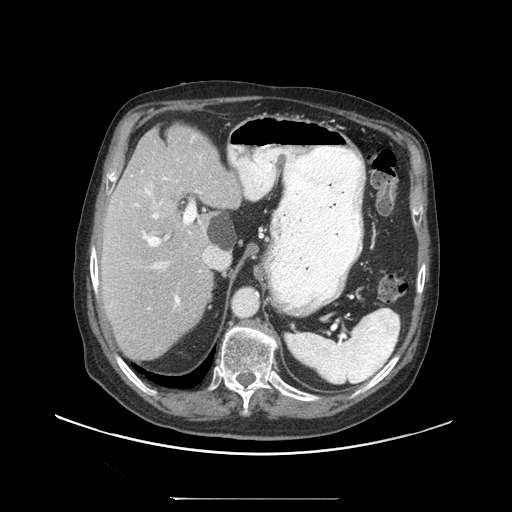
Contrast-enhanced abdominal CT (liver protocol), one axial slice. Slice 67 of 97 in the series (ordered by position). Reconstruction kernel STANDARD. 140 kVp. Soft-tissue window (W 400 / L 40 HU). 2.5 mm slice thickness. 512 × 512 image matrix, field of view 450 × 450 mm. Case-level facts recorded for this patient, not image findings: diagnosis: hepatocellular carcinoma (patient treated with transarterial chemoembolisation; whether this scan precedes or follows treatment is not stated here); TNM stage (as recorded): Stage-IIIC; Child-Pugh class: A; tumour differentiation: well differentiated.
Structures marked on this image (semi-automatically segmented with operator editing):
- abdominal aorta: bounding box [x1, y1, x2, y2] px = [233, 288, 257, 316]
- liver parenchyma outside the tumour (the mass and vessels are separate outlines, so this box may not span the whole liver): [100, 124, 242, 360]
- liver vessels: [135, 137, 202, 307]